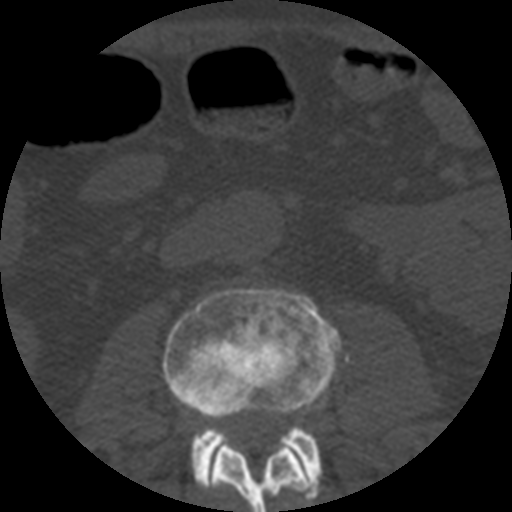
CT including the spine, one axial slice; position 134 of 508 along the scan axis; reconstruction kernel STANDARD; 120 kVp; bone window (W 1800 / L 400 HU); 1.25 mm slice thickness; 512 × 512 image matrix, field of view 160 × 160 mm. Patient age 57 years. From the clinical record (not read from this slice): primary cancer: prostate.
Outlined on this slice (semi-automatically segmented with operator editing):
- L2 vertebra: bounding box <201,430,316,512> (left, top, right, bottom; pixels)
- L3 vertebra: <163,288,339,495>